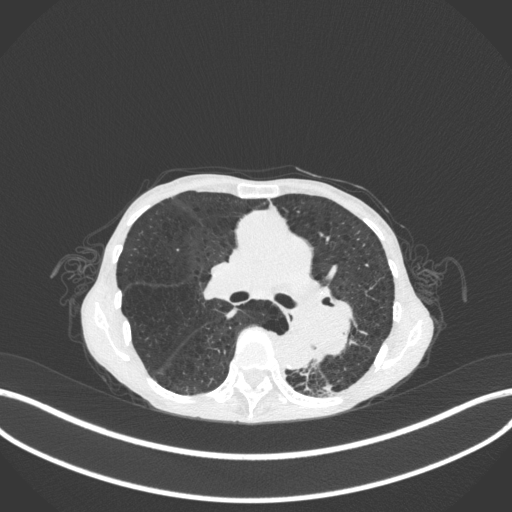
Chest CT, one axial slice. Slice 165 of 347 in the series (ordered by position). Reconstruction kernel B31f. Lung window (W 1500 / L -600 HU). 1 mm slice thickness. 512 × 512 image matrix. Patient: female, 70 years. From the clinical record (not read from this slice): clinical TNM (as recorded): T3 N0 M0; histopathological grade: G3.
Annotated regions visible in this slice (rectangle marked by the reading radiologist):
- lung tumour (recorded histology: small cell carcinoma): bounding box (x1, y1, x2, y2) in pixels: (302, 275, 358, 357)